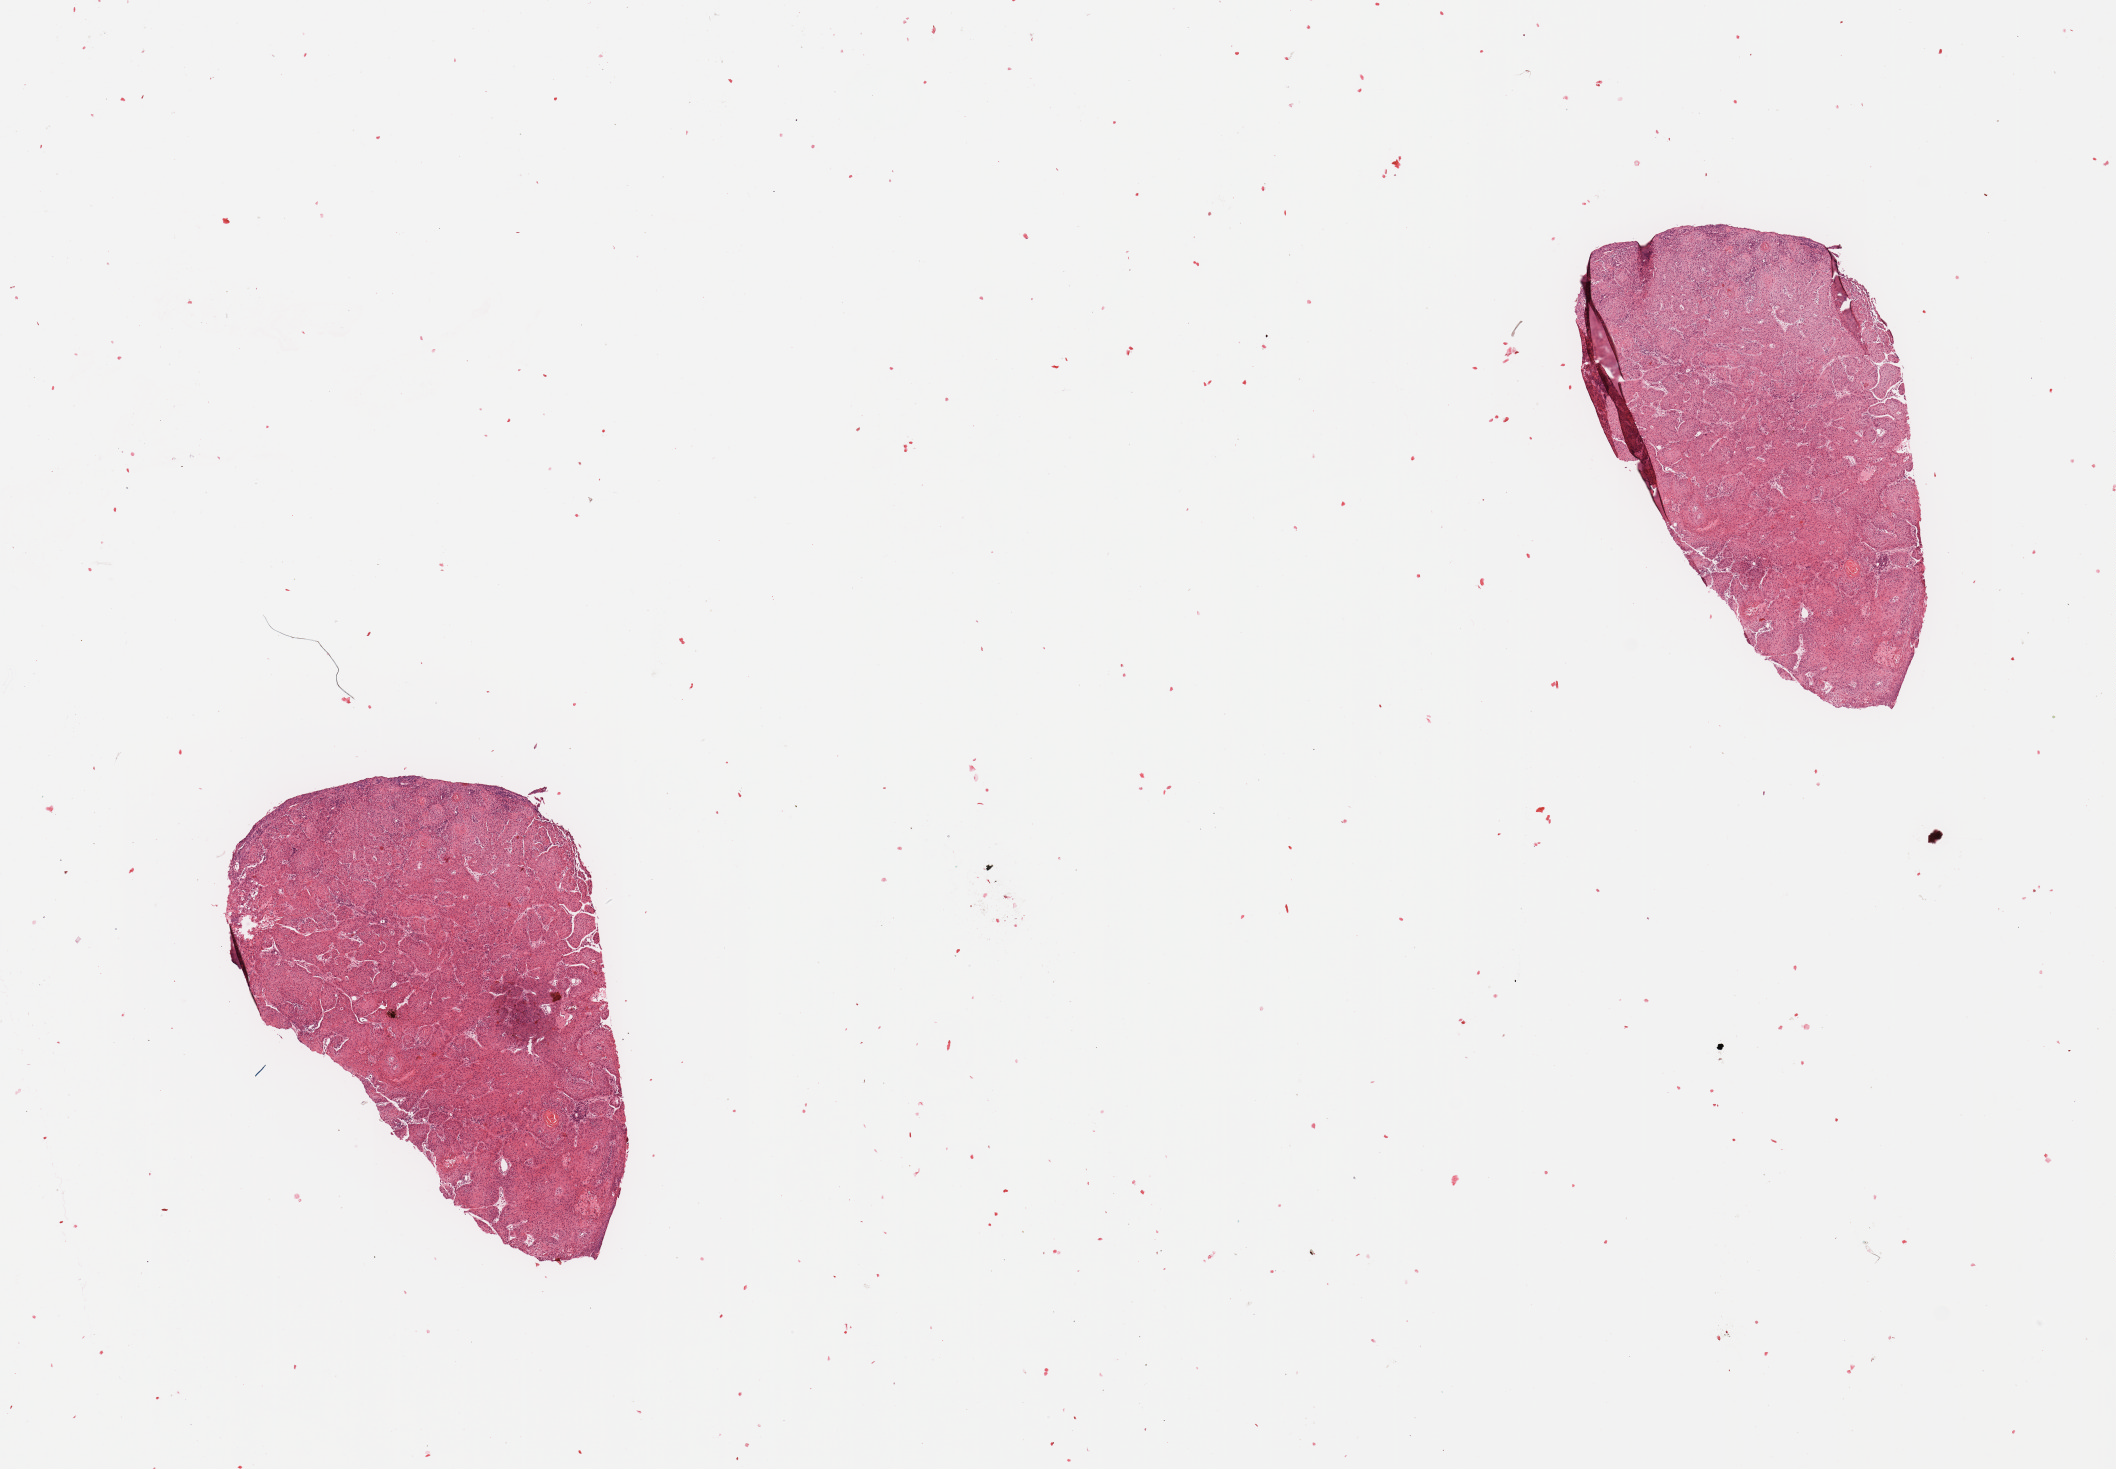
Digitized Hematoxylin and eosin (H&E) stained tissue section (whole slide) — a low-resolution overview of the entire scanned area, about 16.7 x 11.6 mm, tumour tissue sample, sampled site: larynx. Male, 64 y/o. Histologic grade: G2 (moderately differentiated). Slide review estimates, as recorded: tumour nuclei 90%, necrosis 3%.
Primary tumour site (as recorded): larynx. Diagnosis: Squamous cell carcinoma, NOS (larynx, NOS). AJCC pathologic stage: II.